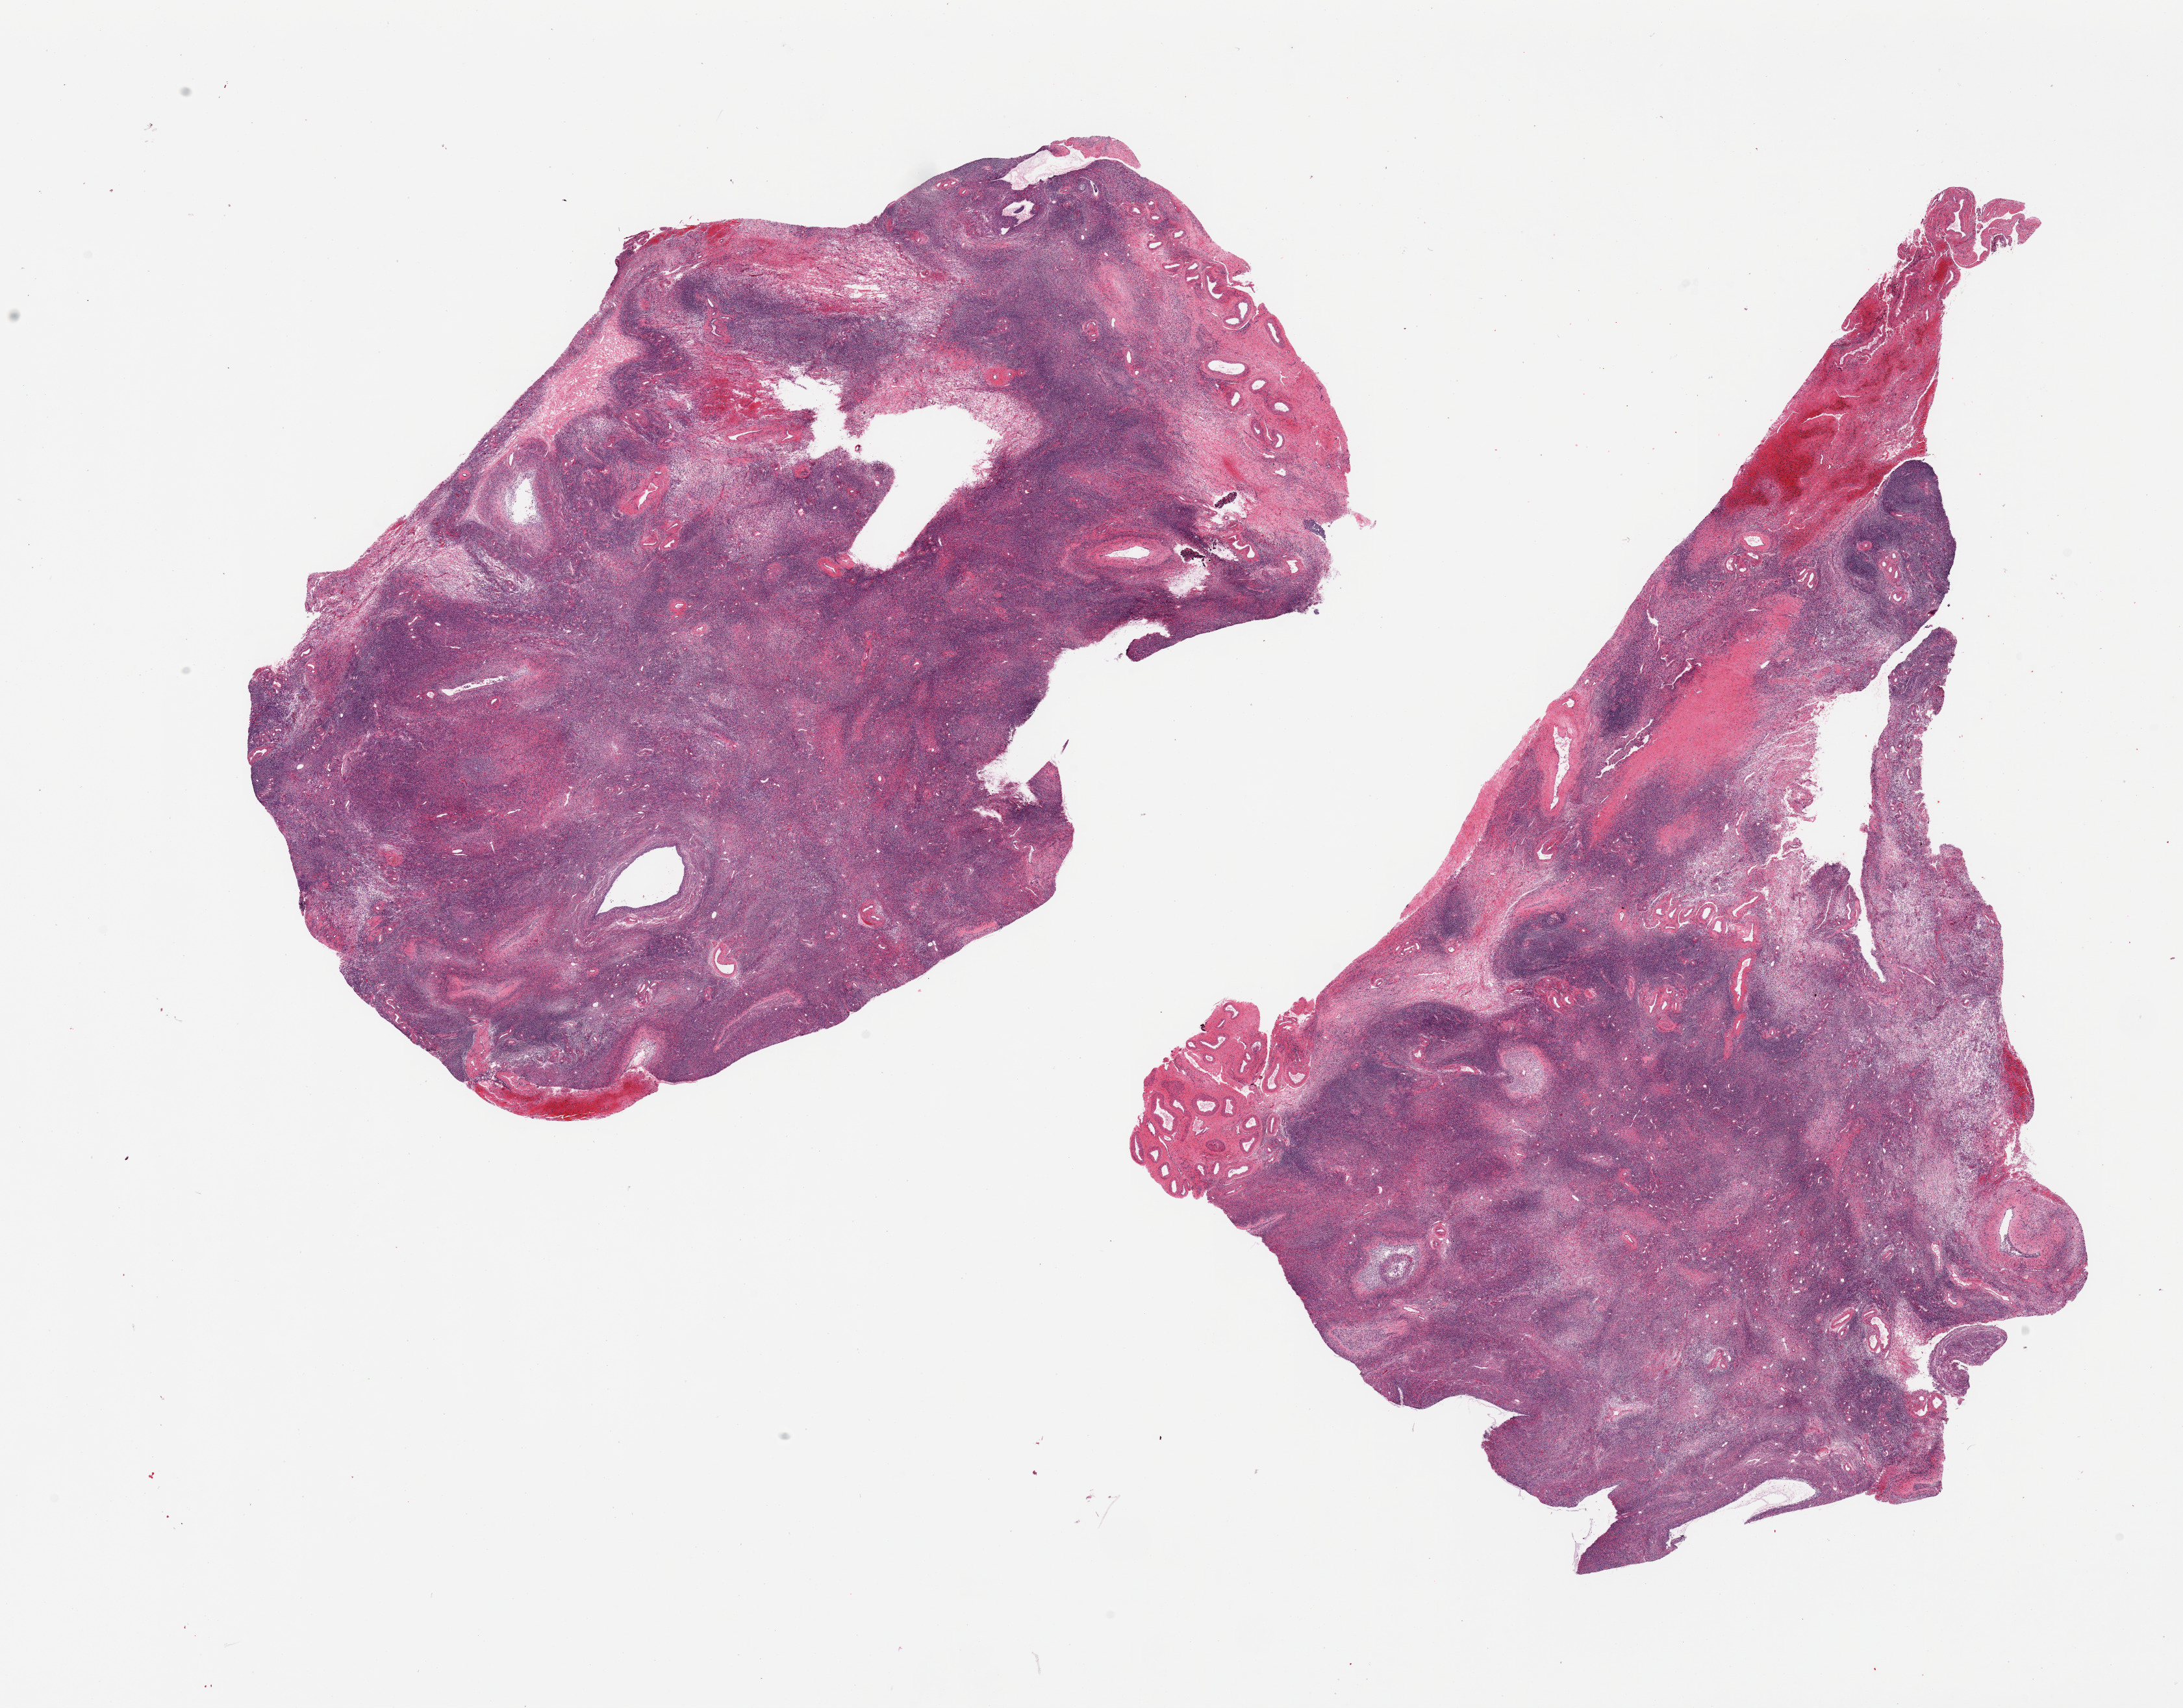
Digitized haematoxylin and eosin-stained section — whole scanned area (about 26.6 x 20.8 mm) shown as a low-resolution overview, PAXgene-fixed, paraffin-embedded tissue, target tissue: ovary, tissue donor sample. Female donor.
Reviewer comment on this tissue sample: 2 pieces.